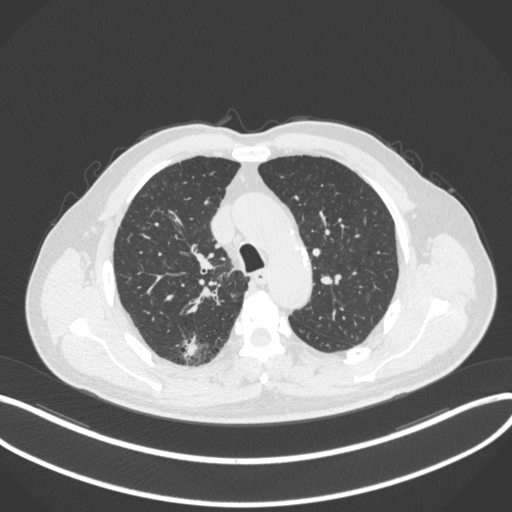
Chest CT, one axial slice; position 271 of 366 along the scan axis; reconstruction kernel B31f; 120 kVp; lung window (W 1500 / L -600 HU); 1 mm slice thickness; 512 × 512 image matrix. Male patient, age 69 years. From the clinical record (not read from this slice): clinical TNM (as recorded): T1b N0 M0.
Annotated regions visible in this slice (rectangle marked by the reading radiologist):
- lung tumour (recorded histology: adenocarcinoma): box from (x=178, y=329) to (x=200, y=364) px